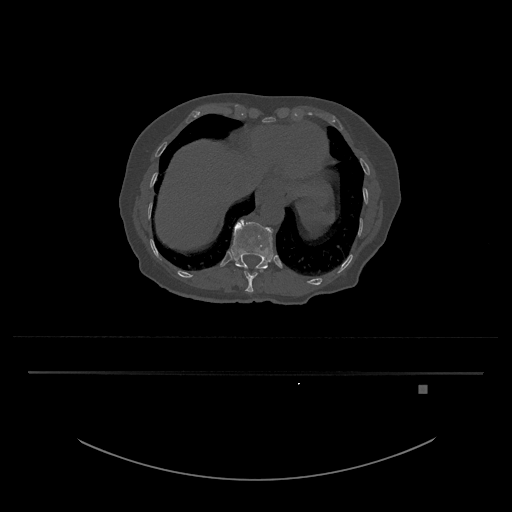
CT including the spine, one axial slice; slice 634 of 797 in the series (ordered by position); reconstruction kernel Br40s/3; 120 kVp; bone window (W 1800 / L 400 HU); 0.5 mm slice thickness; 512 × 512 image matrix, field of view 500 × 500 mm. Female patient, age 57 years. From the clinical record (not read from this slice): primary cancer: cervical.
Outlined on this slice (semi-automatic segmentation, software-assisted and operator-edited):
- T11 vertebra: bounding box <244,267,265,292> (left, top, right, bottom; pixels)
- T12 vertebra: <231,220,274,270>